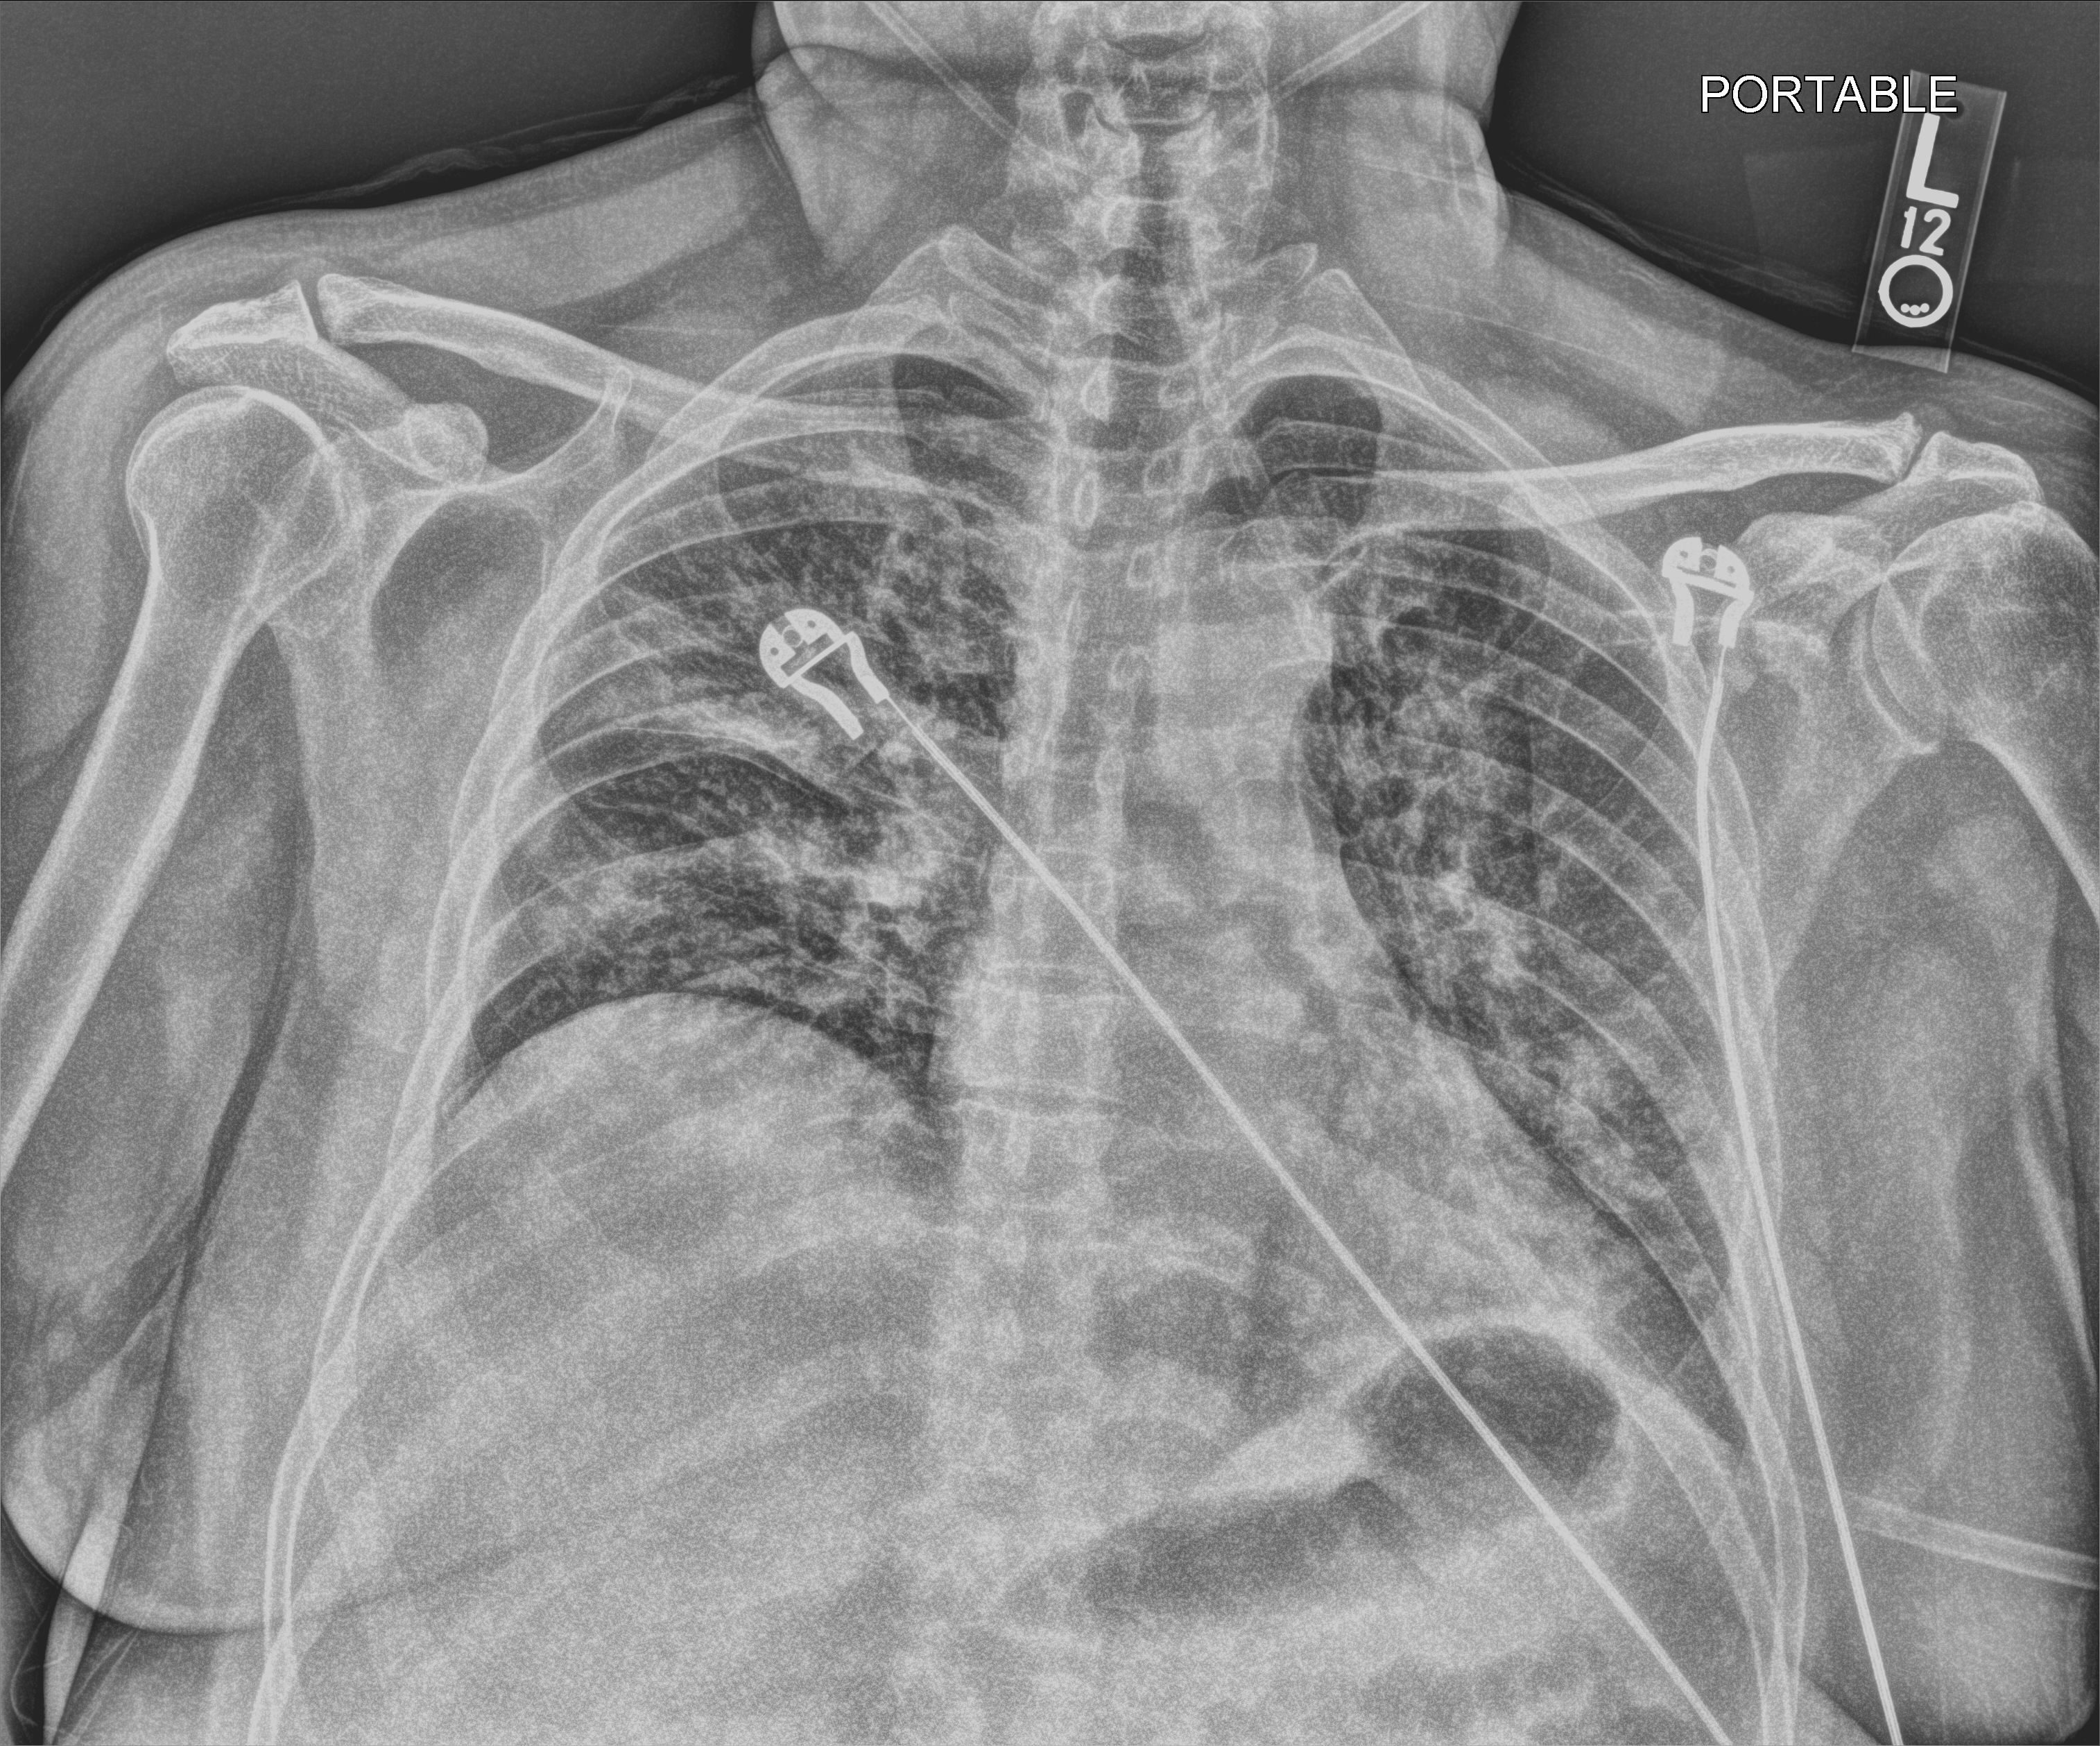
Bedside chest radiograph (computed radiography), anteroposterior (AP) projection. Male patient hospitalised with COVID-19, age 18–59 years.
Hospital-stay facts (about this admission, not read from this image; timing relative to this image not recorded): admitted to intensive care during this hospital stay: yes; COPD (admission record): no.